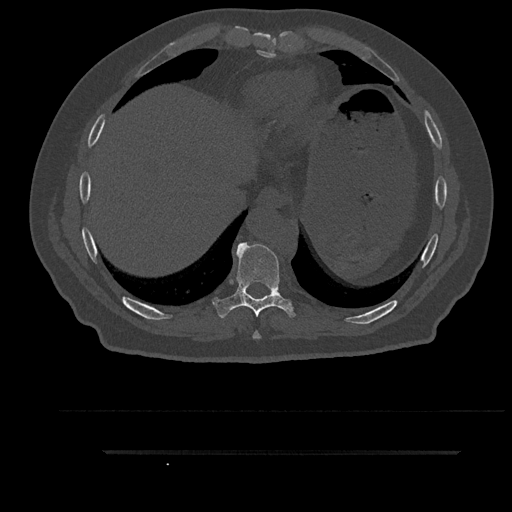
CT including the spine, one axial slice. Position 426 of 797 along the scan axis. Bone window (W 1800 / L 400 HU). 512 × 512 image matrix, field of view 432 × 432 mm. Patient: male, 63 years. Case-level facts recorded for this patient, not image findings: primary cancer: renal.
Annotated regions visible in this slice (semi-automatically segmented with operator editing):
- T8 vertebra: bounding box <253,331,261,339> (left, top, right, bottom; pixels)
- T9 vertebra: <213,242,295,318>